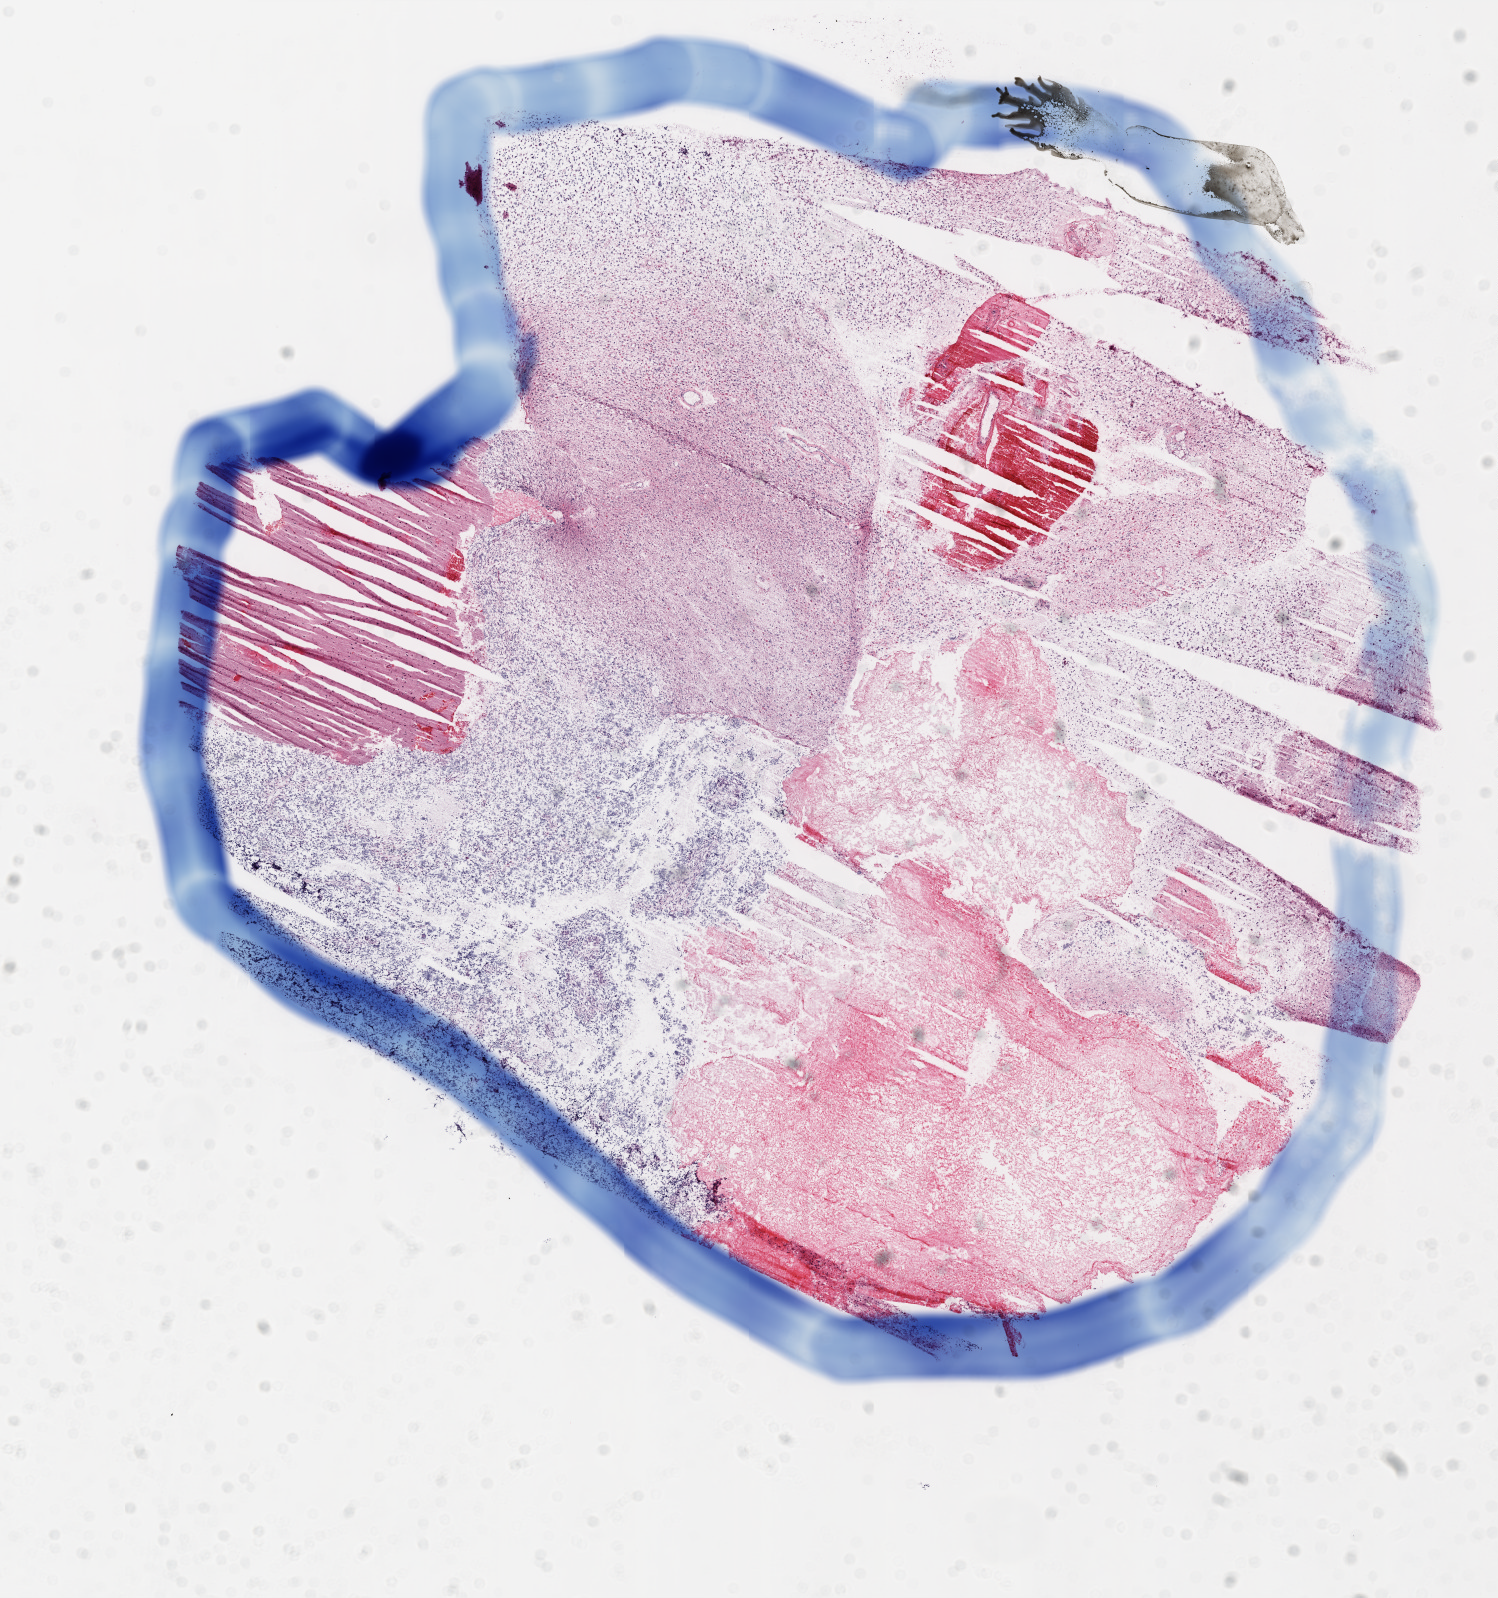
Whole-slide histology image, H&E-stained, shown as a low-resolution overview of the whole scanned area (about 12.0 x 12.8 mm, slide scanned at 20x). Frozen section from the top of the tissue portion. Primary tumour sample from the brain. Female patient; age at initial diagnosis 33 years. Slide review estimates, as recorded: tumour cells 90%, tumour nuclei 95%, normal cells 10%, stromal cells 0%, necrosis 0%. Inflammatory infiltration, as recorded: lymphocyte infiltration 0%, monocyte infiltration 0%, neutrophil infiltration 0%.
- pathologic diagnosis: Glioblastoma